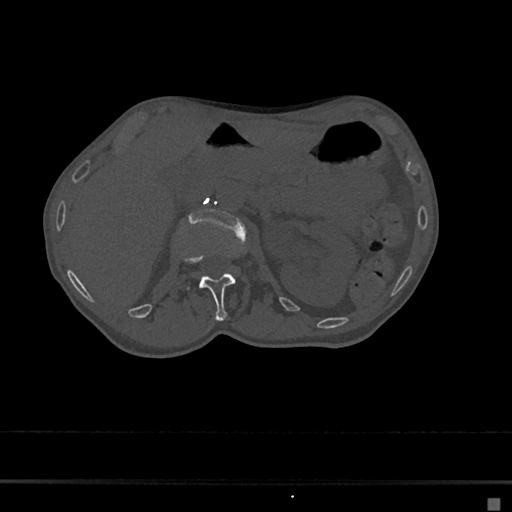
CT including the spine, one axial slice. Position 57 of 797 along the scan axis. 120 kVp. Bone window (W 1800 / L 400 HU). 512 × 512 image matrix, field of view 360 × 360 mm. Female patient, age 68 years. From the clinical record (not read from this slice): primary cancer: renal.
Structures marked on this image (semi-automatically segmented with operator editing):
- L1 vertebra: bounding box [x1, y1, x2, y2] px = [178, 252, 248, 320]
- L2 vertebra: [189, 208, 243, 231]